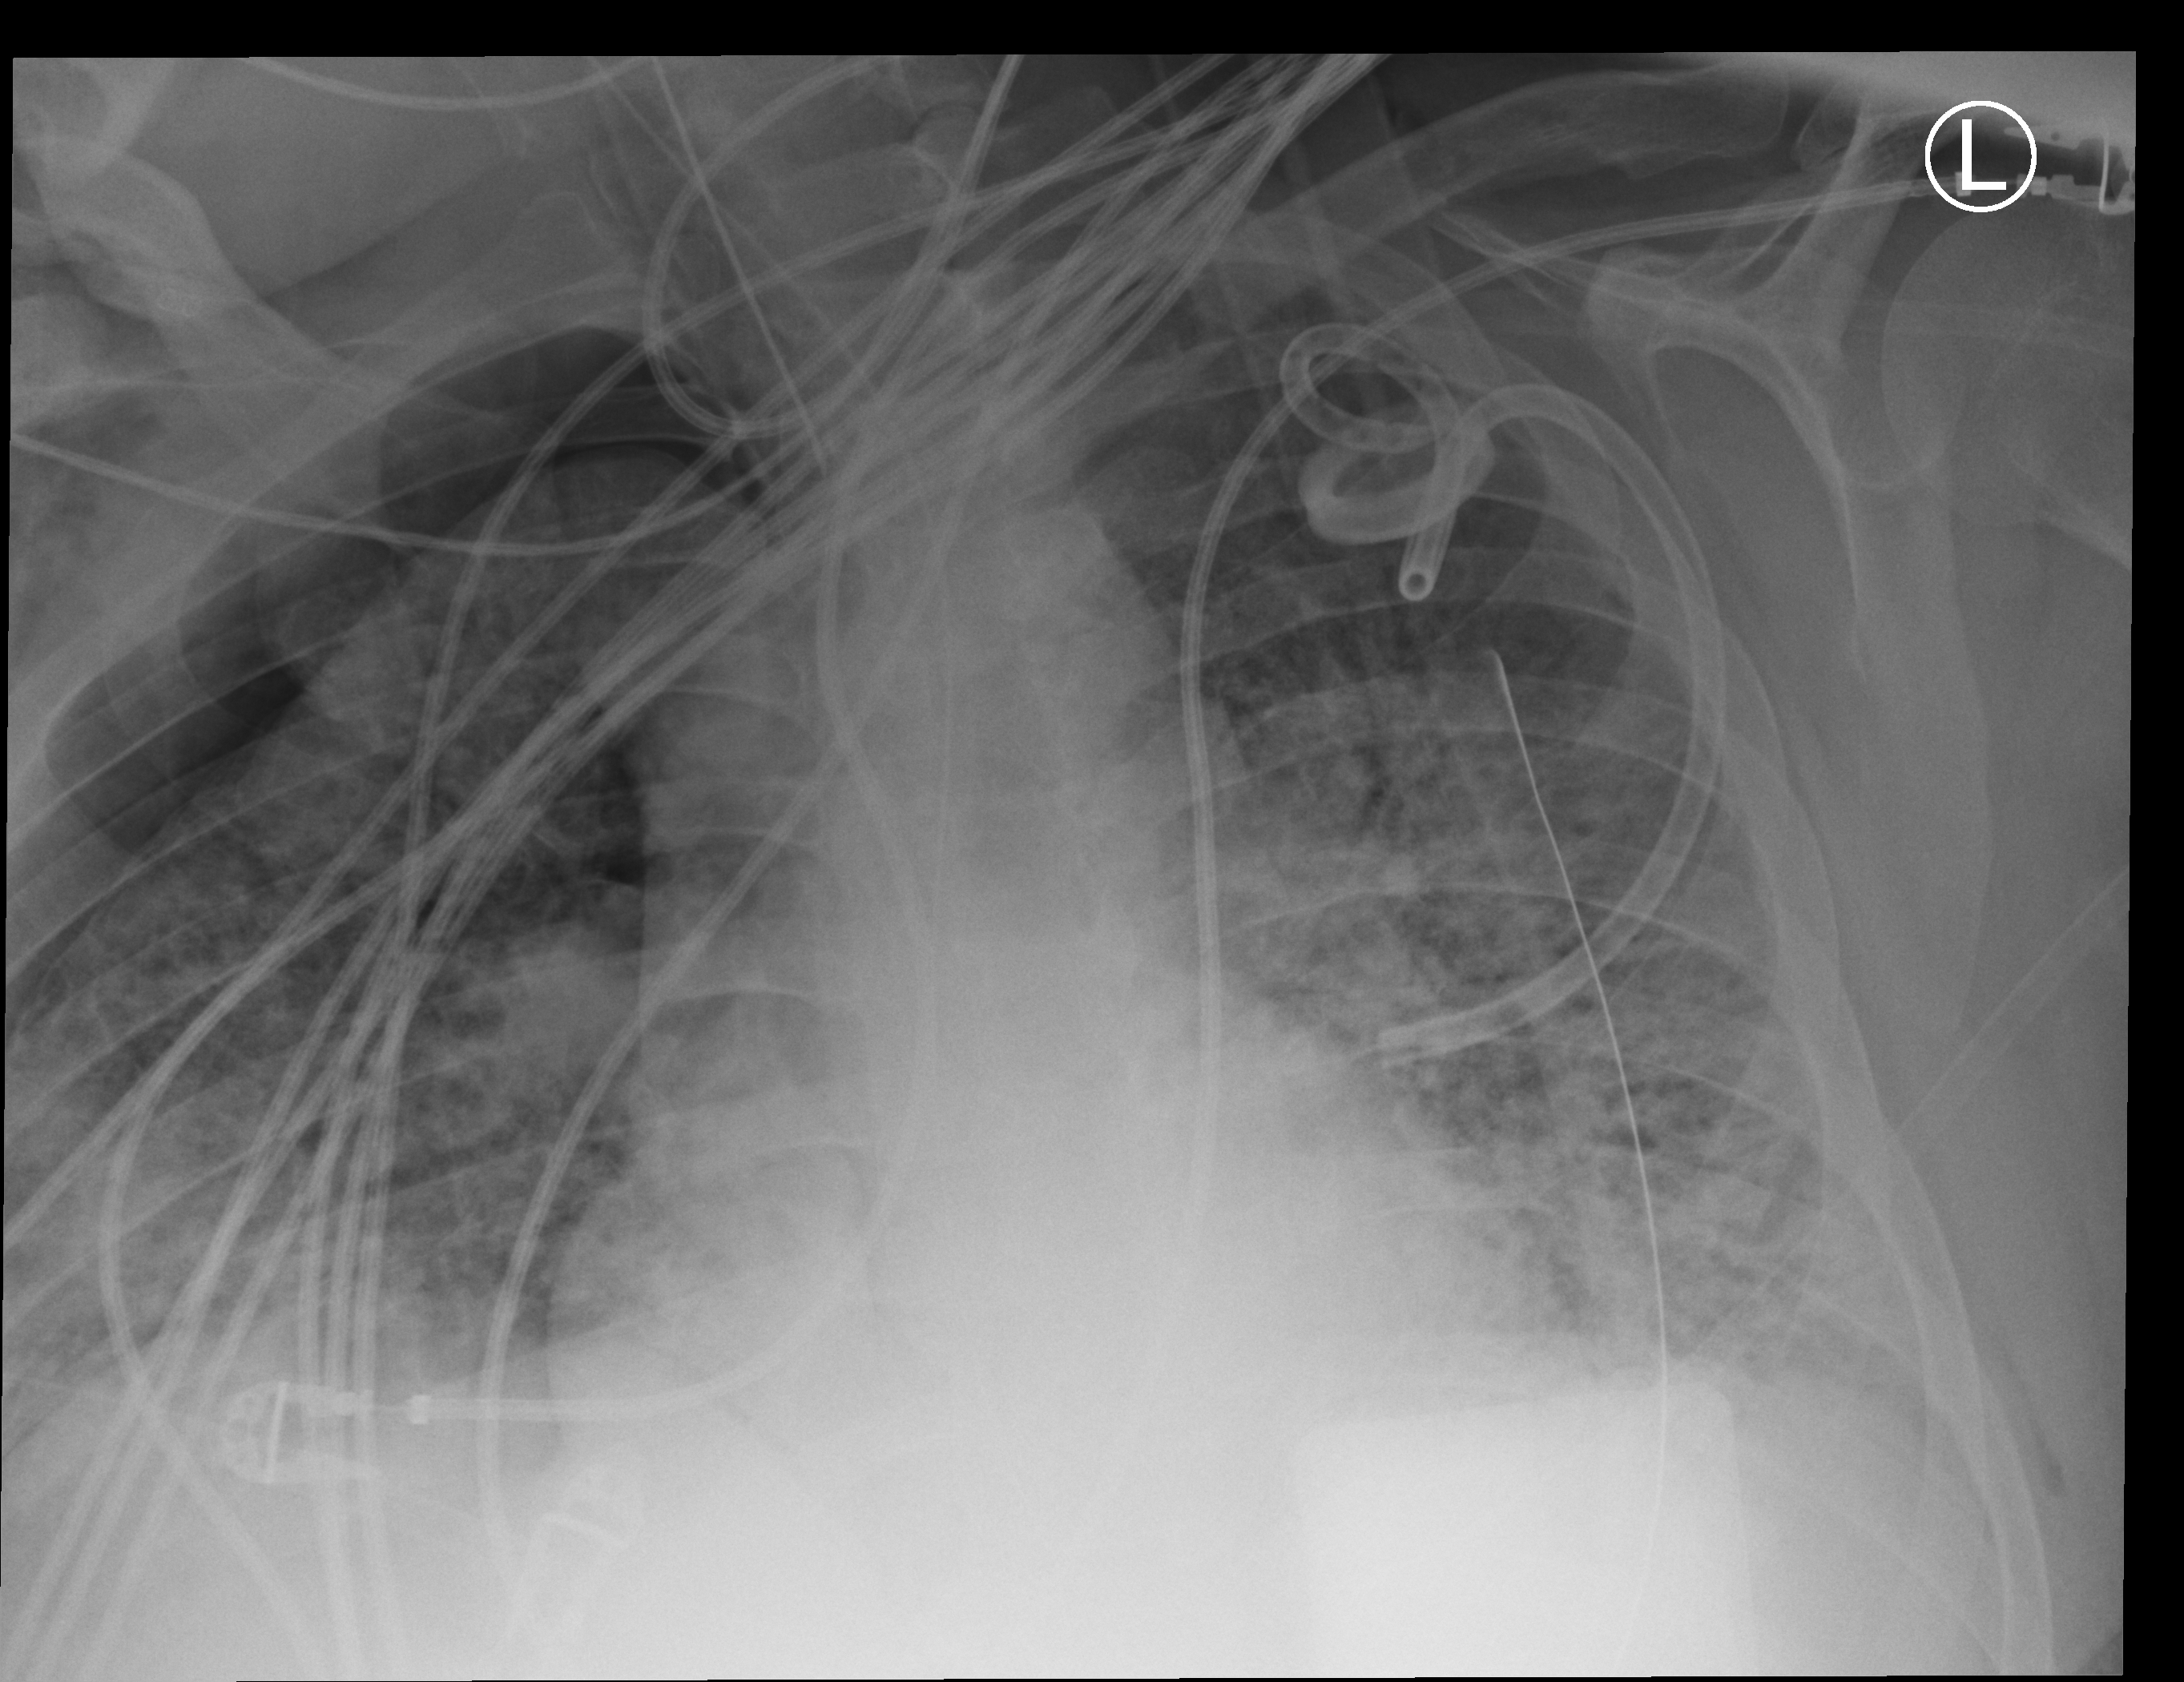
Portable chest radiograph, anteroposterior (AP) projection. Adult patient hospitalised with COVID-19, age 18–59 years.
Hospital-stay facts (about this admission, not read from this image; timing relative to this image not recorded): mechanically ventilated during this hospital stay: yes; length of hospital stay: 31 days; admitted to intensive care during this hospital stay: yes.